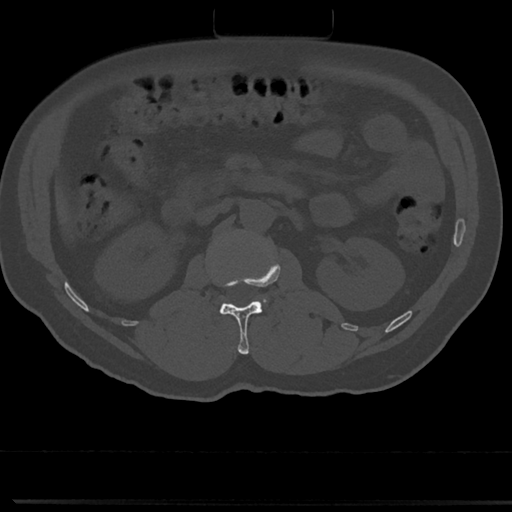
CT including the spine, one axial slice. Position 58 of 817 along the scan axis. Reconstruction kernel Br40s/3. 120 kVp. Bone window (W 1800 / L 400 HU). 0.5 mm slice thickness. 512 × 512 image matrix, field of view 355 × 355 mm. Patient: male, 61 years. From the clinical record (not read from this slice): primary cancer: prostate.
Annotated regions visible in this slice (semi-automatic segmentation, software-assisted and operator-edited):
- L1 vertebra: bounding box (x1, y1, x2, y2) in pixels: (214, 257, 280, 354)